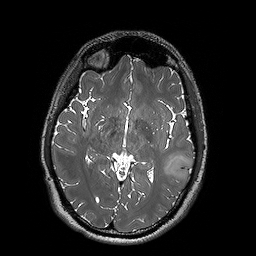
Brain MRI from a brain-tumour surgery series, one axial slice. Position 93 of 192 along the scan axis. 1 mm slice thickness. 256 × 256 image matrix, field of view 250 × 250 mm. From the clinical record (not read from this slice): histopathology: Oligodendroglioma; WHO grade: 2; IDH mutation: yes.
Outlined on this slice (expert manual segmentation):
- tumour: bounding box [x1, y1, x2, y2] px = [159, 155, 193, 182]